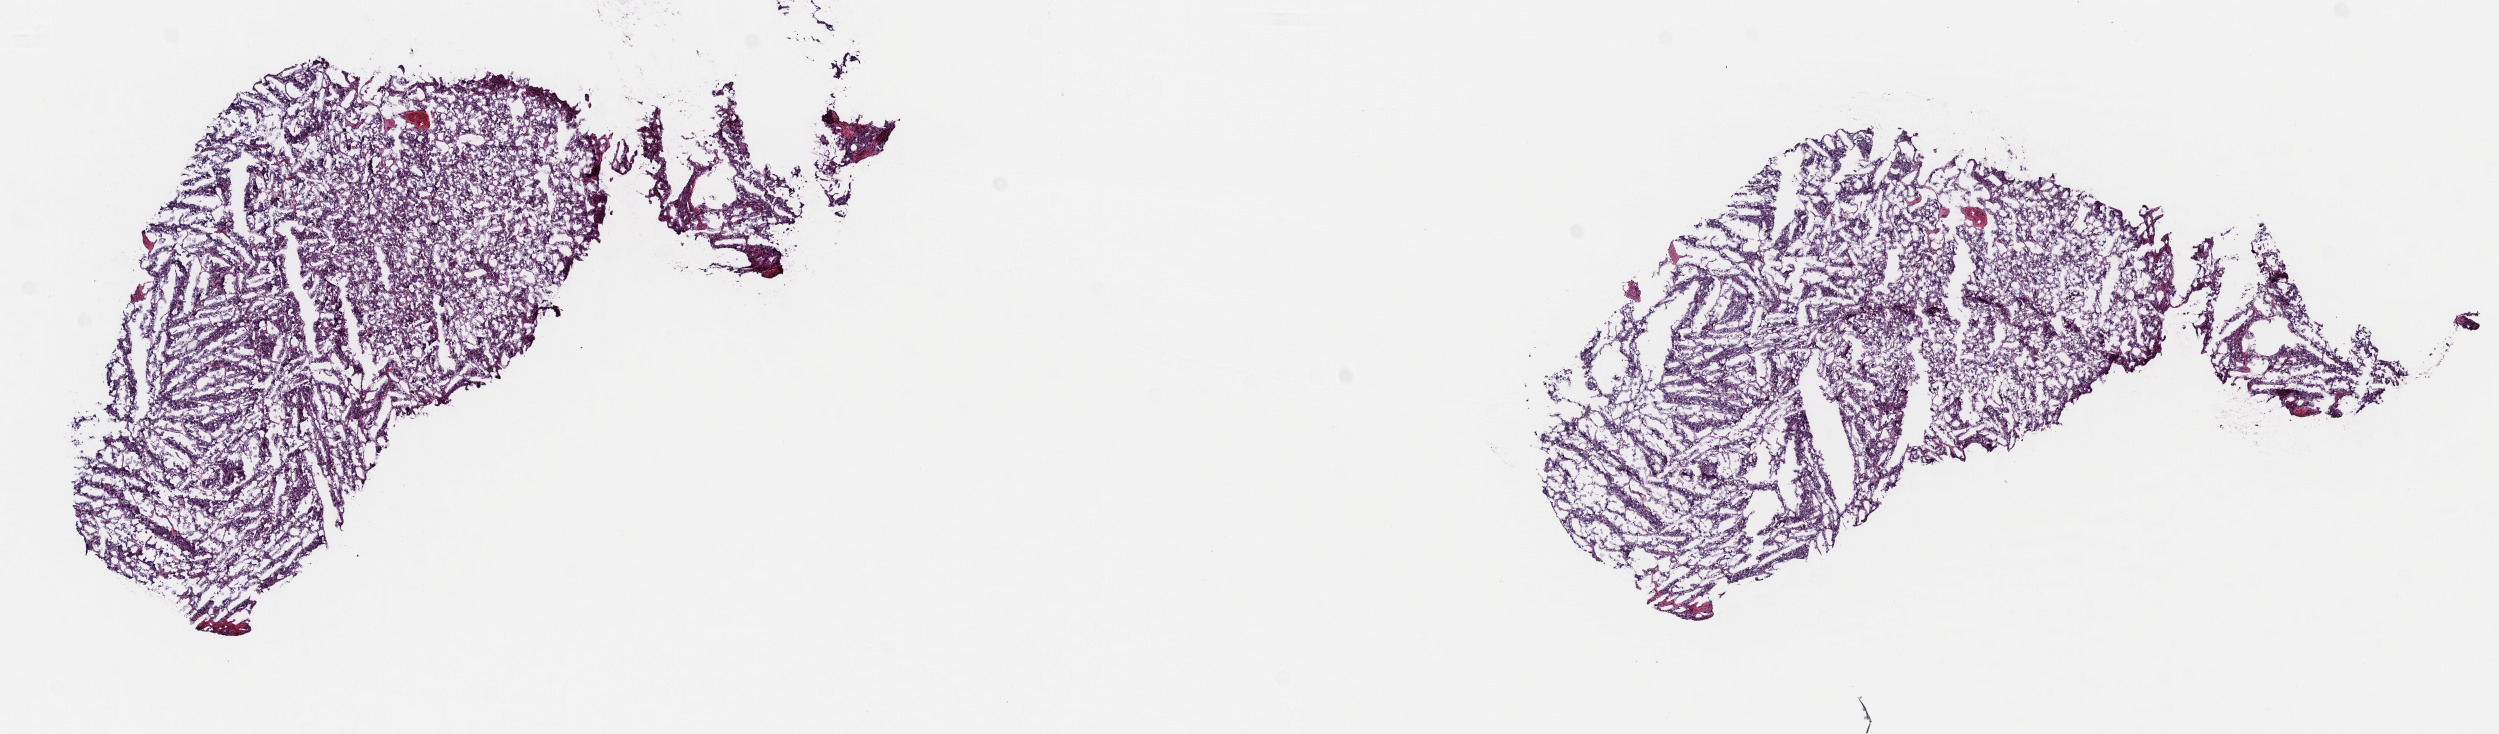
Hematoxylin and eosin (H&E) stained whole-slide image — a low-resolution overview of the entire scanned area, about 19.6 x 5.8 mm (slide scanned at 40x), frozen section, primary tumour sample from the adrenal gland. Male patient; age at initial diagnosis 62 years. Pathologist review of this section (percent, as recorded): tumour cells 100%, tumour nuclei 80%, normal cells 0%, stromal cells 0%, necrosis 0%. Inflammatory infiltration, as recorded: lymphocyte infiltration 1%, monocyte infiltration 0%, neutrophil infiltration 0%.
Pathologic diagnosis: Pheochromocytoma, malignant. Lymph nodes positive (case pathology): 2 of 2 examined.